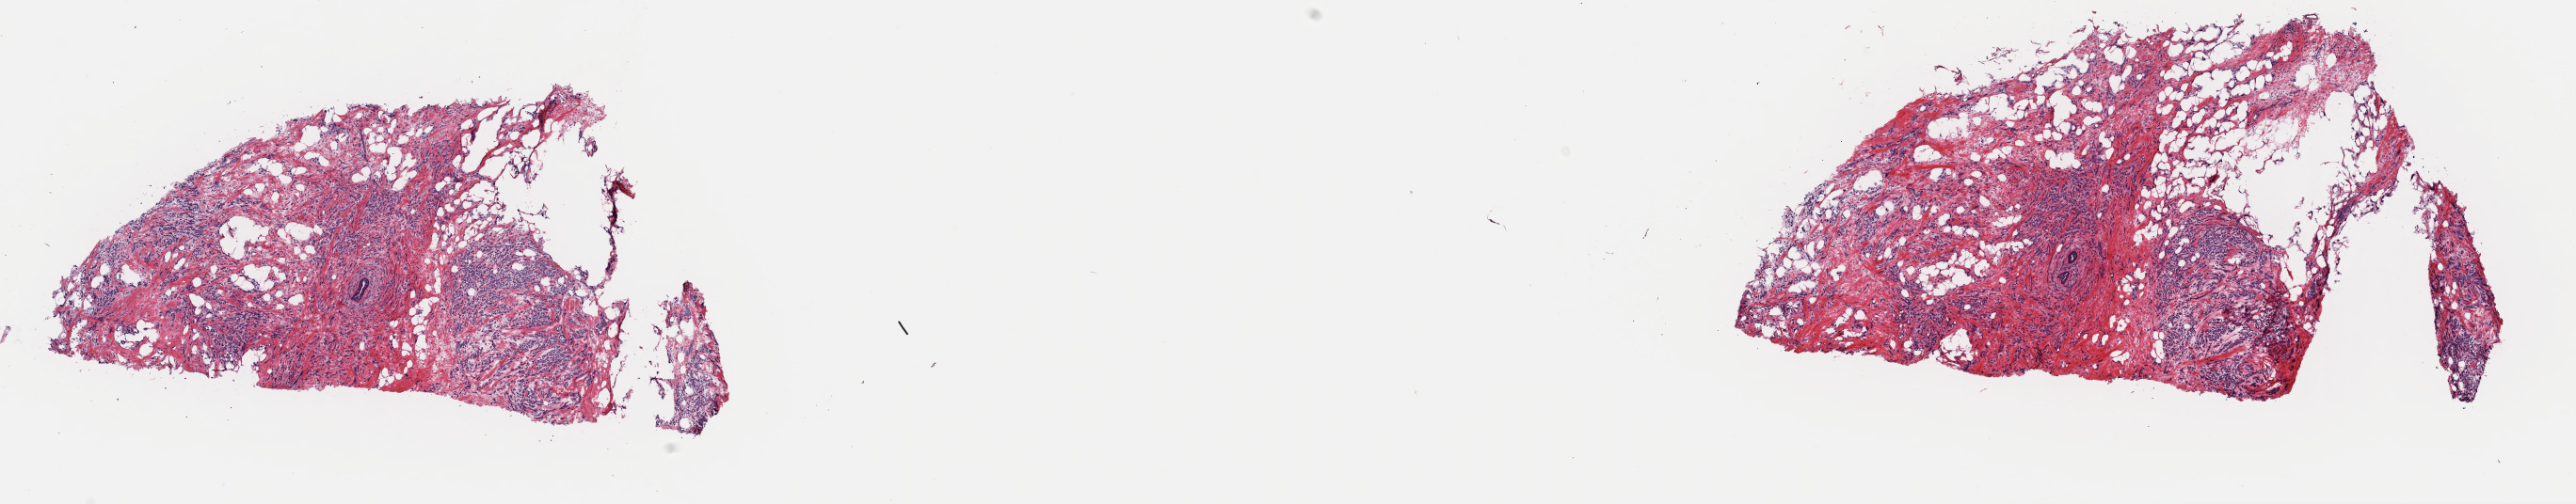
H&E whole-slide image — shown as a low-resolution overview of the whole scanned area (about 21.6 x 4.2 mm, acquisition: 40x scan). Frozen section from the top of the tissue portion. Primary tumour sample from the breast. Female, age 49 years at initial diagnosis. Pathologist review of this section (percent, as recorded): tumour cells 100%, tumour nuclei 75%, normal cells 0%, stromal cells 0%, necrosis 0%. Inflammatory infiltration, as recorded: lymphocyte infiltration 2%, monocyte infiltration 0%, neutrophil infiltration 0%.
- AJCC pathologic stage: IIIC
- lymph nodes positive (case pathology): 19 of 21 examined
- diagnosis: Lobular carcinoma, NOS
- laterality: left